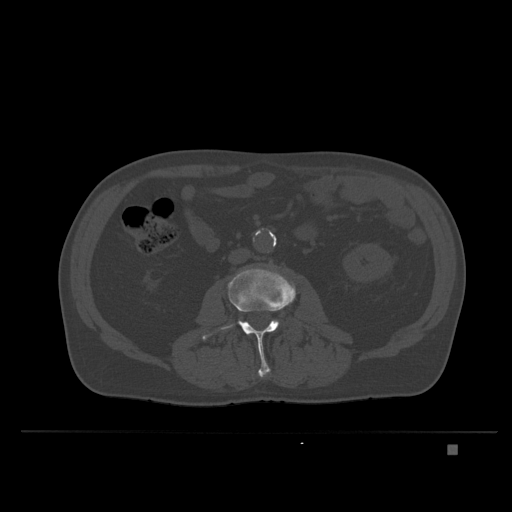
CT including the spine, one axial slice. Position 95 of 435 along the scan axis. Bone window (W 1800 / L 400 HU). 1.5 mm slice thickness. 512 × 512 image matrix, field of view 434 × 434 mm. Patient: male, 73 years. Case-level facts recorded for this patient, not image findings: primary cancer: skin.
Structures marked on this image (semi-automatic segmentation, software-assisted and operator-edited):
- L2 vertebra: bounding box [x1, y1, x2, y2] px = [258, 371, 270, 377]
- L3 vertebra: [202, 266, 296, 376]